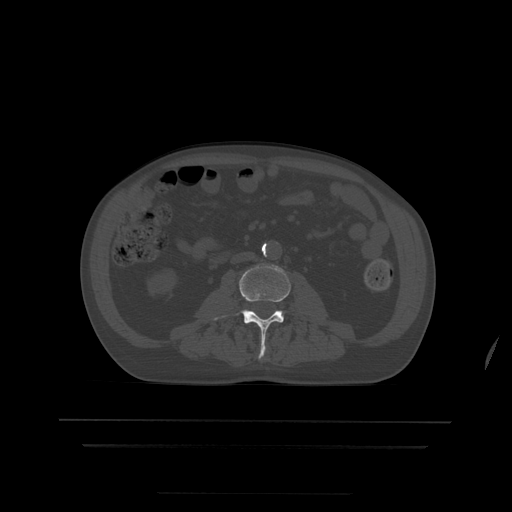
CT including the spine, one axial slice. Bone window (W 1800 / L 400 HU). 512 × 512 image matrix, field of view 436 × 436 mm. Patient age 68 years. Case-level facts recorded for this patient, not image findings: primary cancer: urothelial.
Structures marked on this image (semi-automatic segmentation, software-assisted and operator-edited):
- L3 vertebra: bounding box <214,266,291,359> (left, top, right, bottom; pixels)